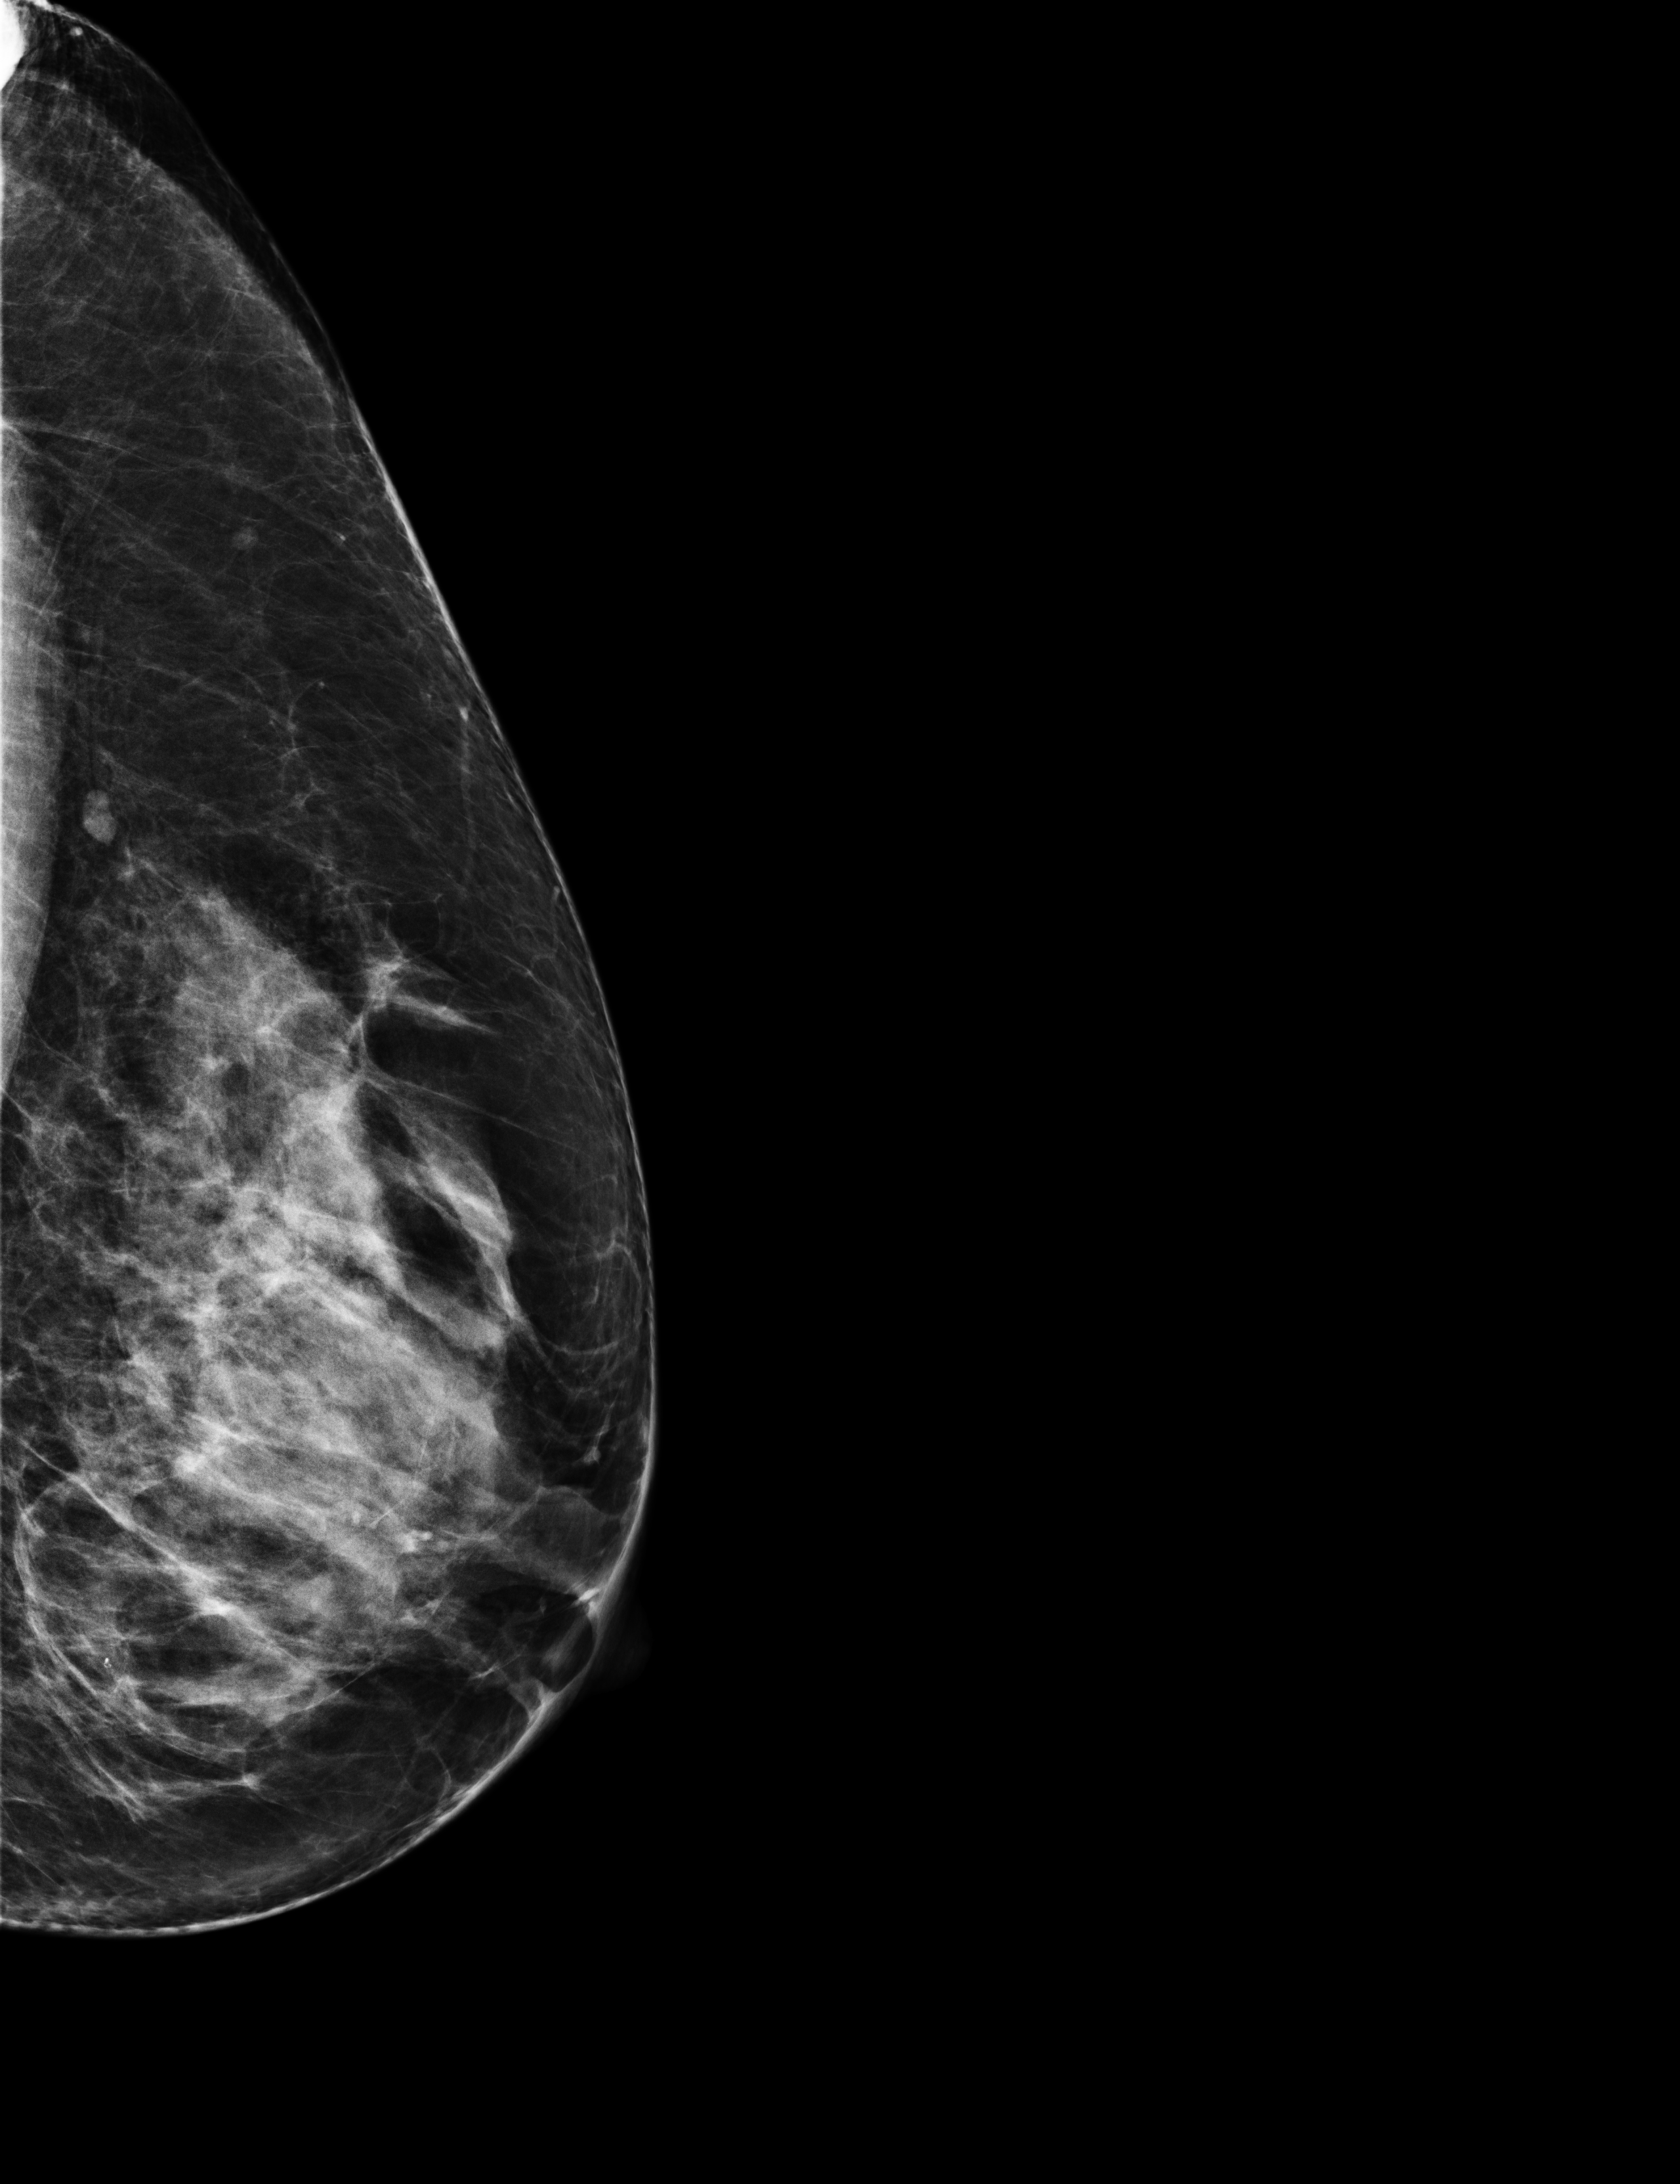
Digital mammogram (FFDM); left breast; laterally exaggerated craniocaudal (XCCL) view; screening examination; compressed breast thickness 65 mm. Patient aged 59 years (female).
BI-RADS breast density category at the screening exam (both breasts, scale 1–4): 3. Final BI-RADS assessment for this screening round (tomosynthesis exam, both breasts): category 2. Recall: no recall after this screen.